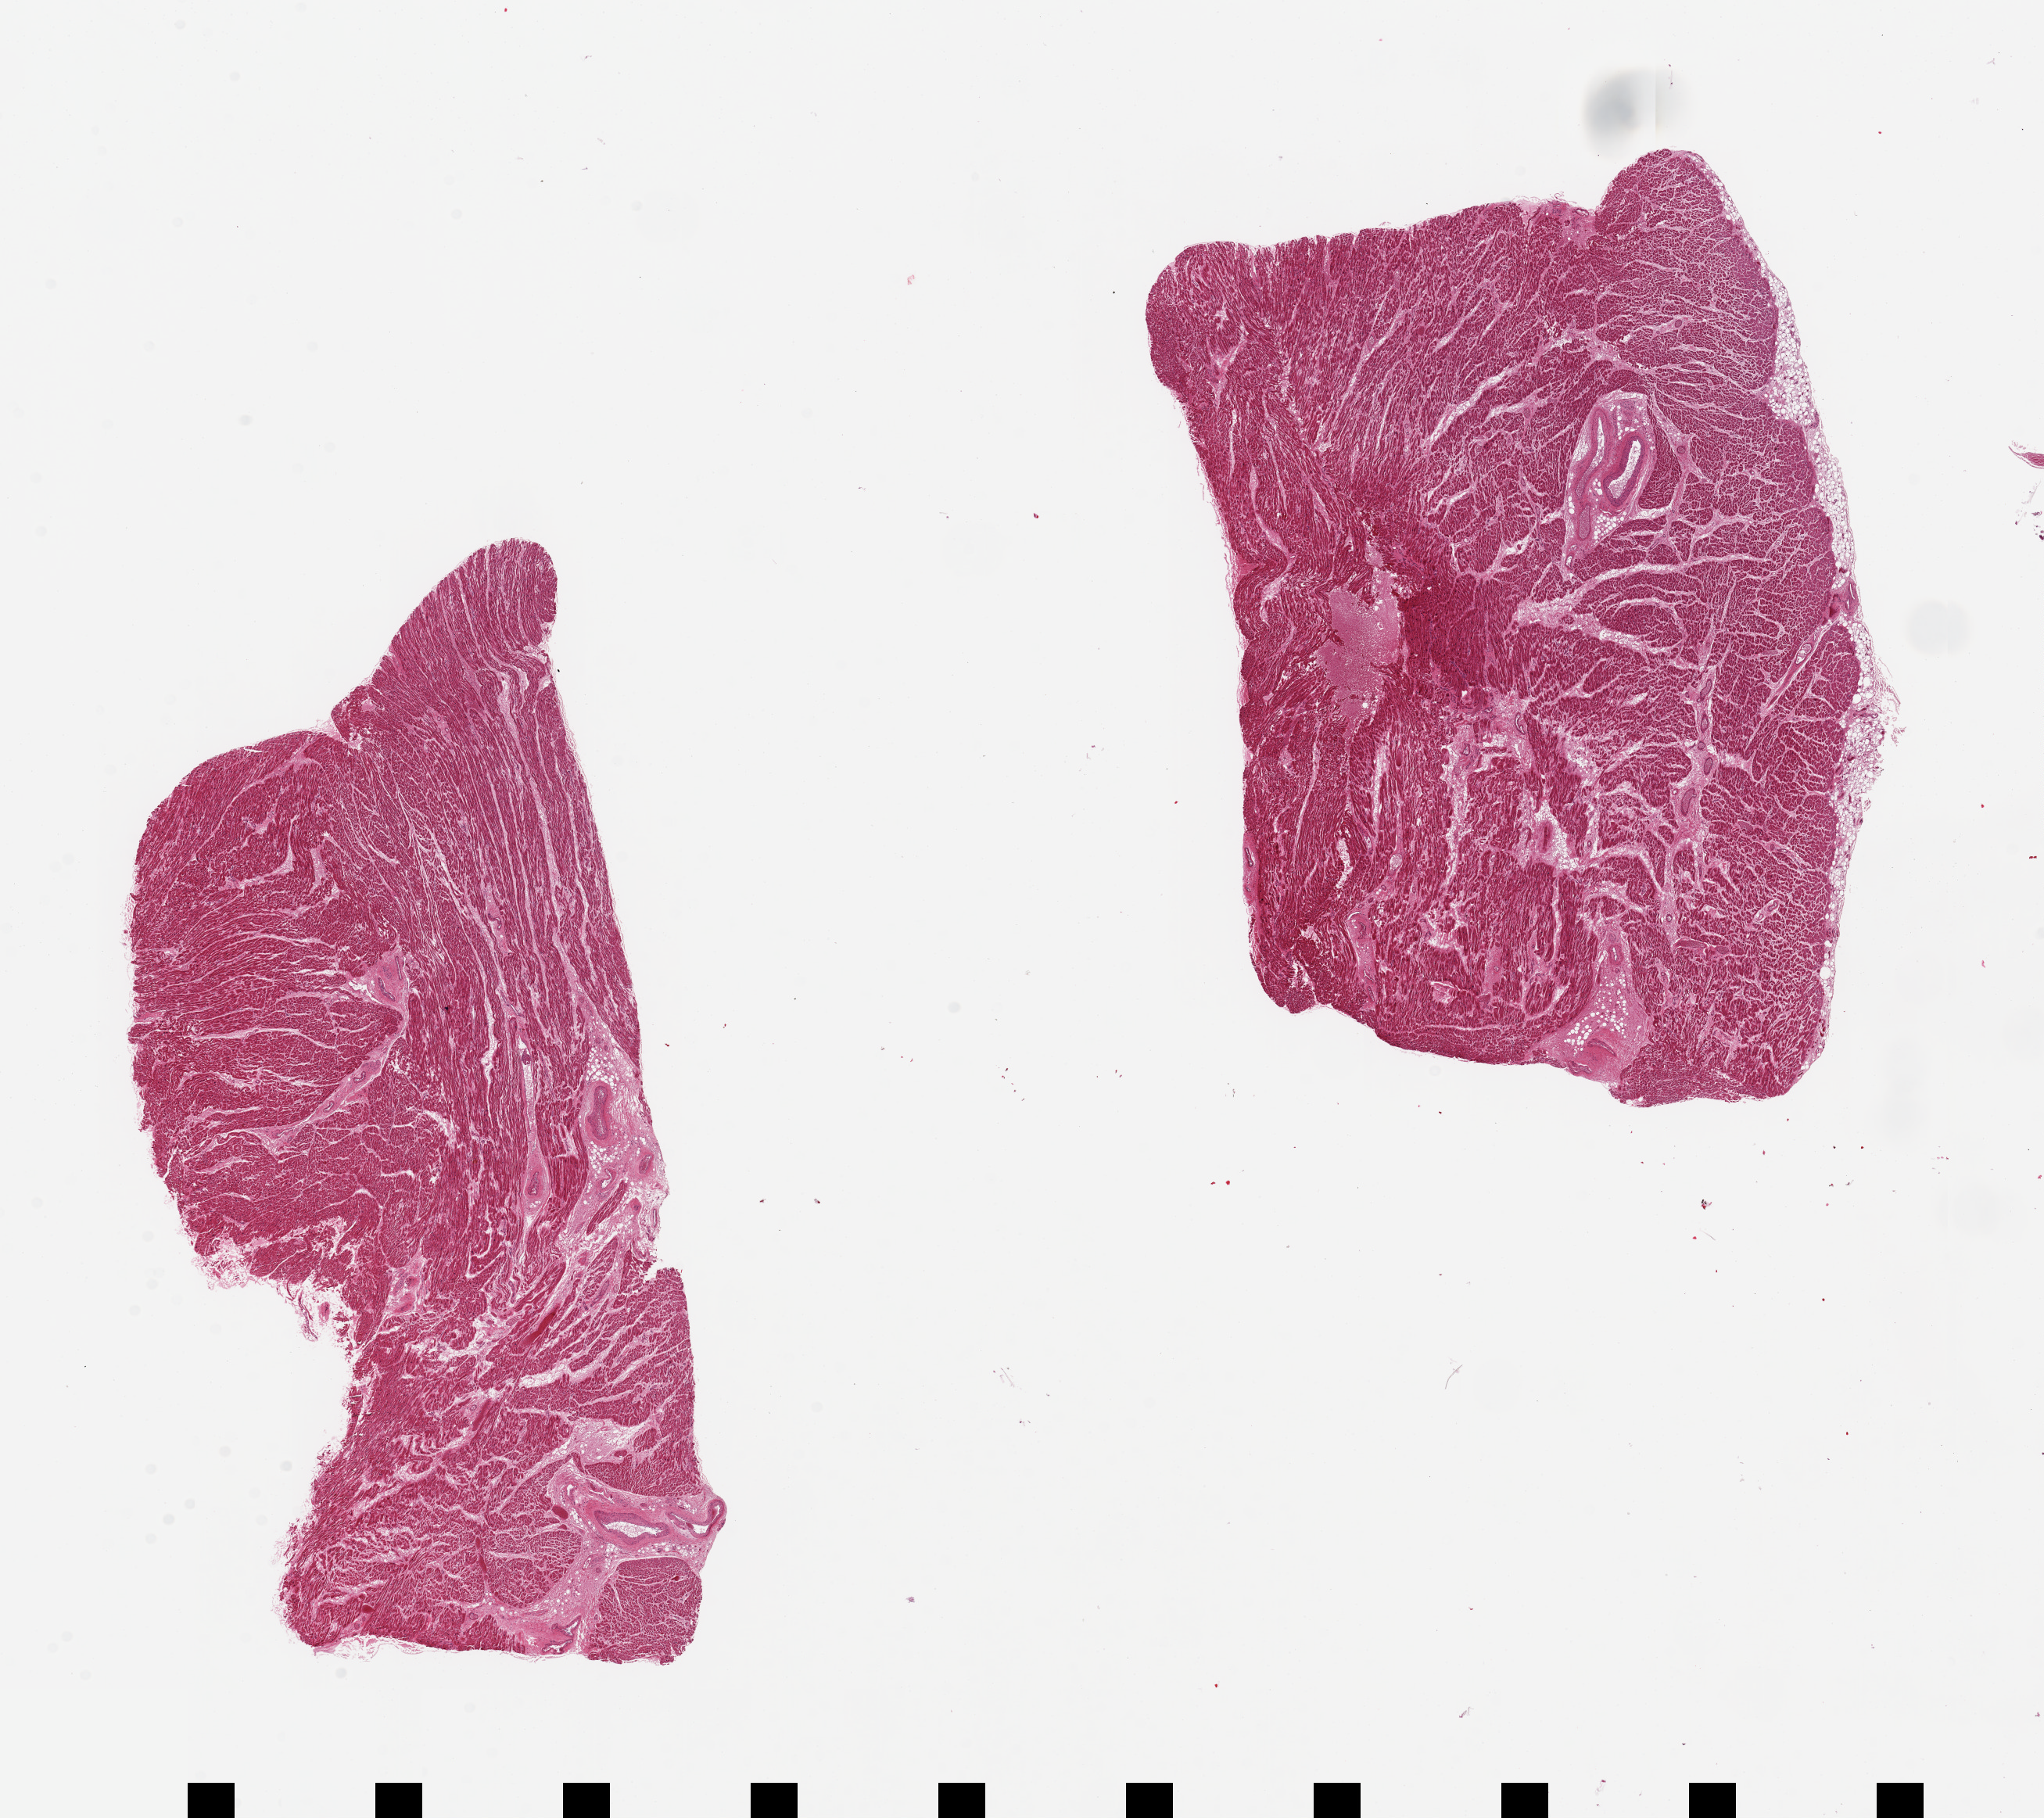
Whole-slide image, H&E stain — low-resolution overview of the scanned area, about 20.7 x 18.4 mm, PAXgene-fixed paraffin-embedded (PFPE) section, target tissue: heart, donor tissue sample. Donor: male.
Pathologist's review note for this sample: 2 pieces; focus of myocardial hypereosinophilia next to a 1.5 mm hemorrhage (possible early infarct); 0.4 mm fat on one edge.